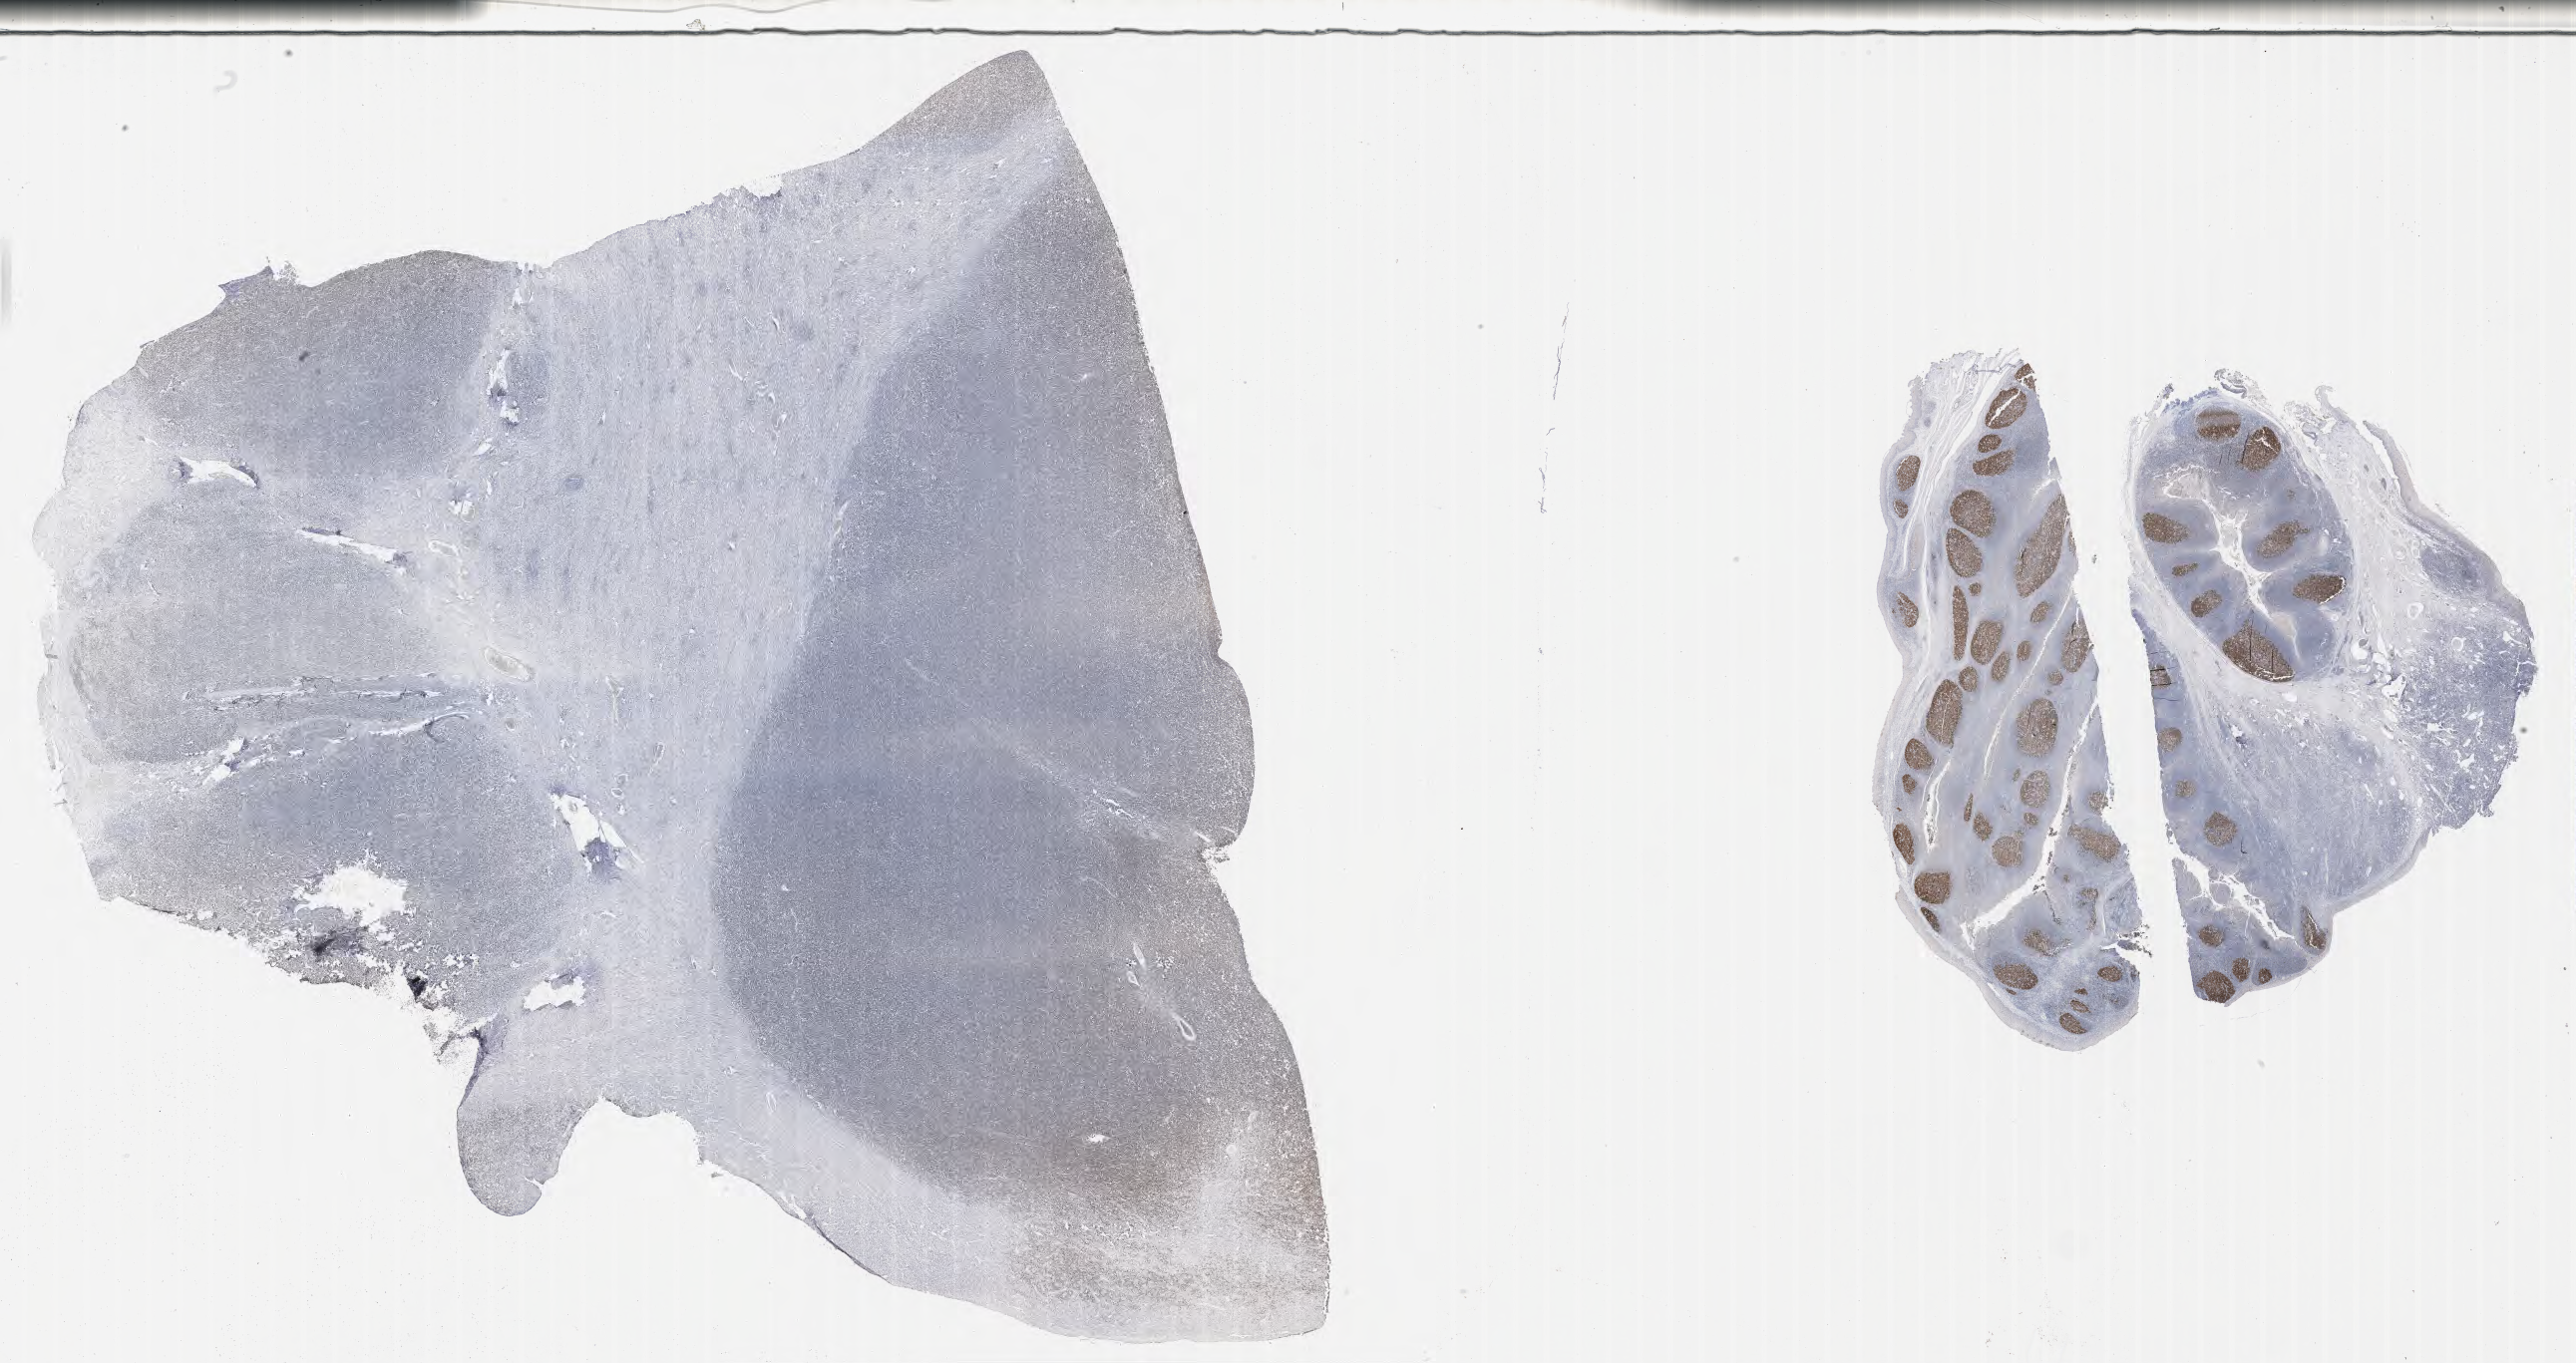
Immunohistochemistry (IHC) whole-slide image stained for BCL6, shown as a low-resolution overview of the whole scanned area (about 41.7 x 22.1 mm). Specimen: tumor tissue. Female, age 8 years at initial diagnosis.
- histologic diagnosis: Burkitt lymphoma, NOS